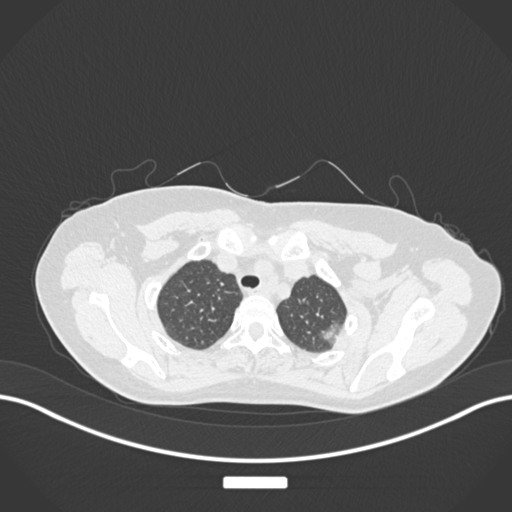
Chest CT, one axial slice; position 148 of 181 along the scan axis; reconstruction kernel B30f; lung window (W 1500 / L -600 HU); 512 × 512 image matrix. Patient: female, 58 years. From the clinical record (not read from this slice): clinical TNM (as recorded): T1c N0 M0.
Annotated regions visible in this slice (bounding box drawn by a radiologist):
- lung tumour (recorded histology: adenocarcinoma): box from (x=317, y=316) to (x=344, y=346) px